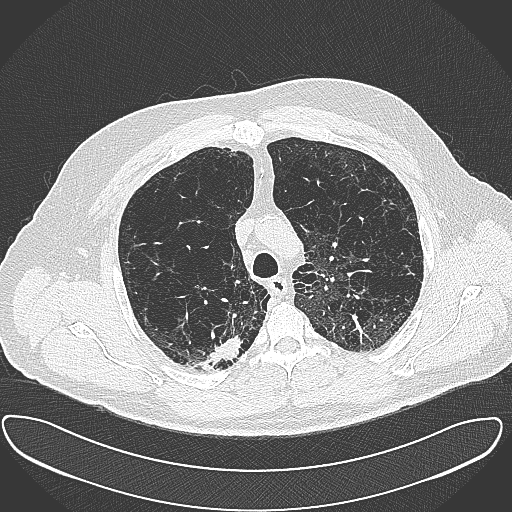
Chest CT (low-dose screening protocol), one axial image, baseline annual screen, lung window (W 1500 / L -600 HU), 1 mm slice thickness, lung (sharp) reconstruction kernel (B80f), slice 90 of 385 in the series. Male participant, aged 60 years at enrolment. Current smoker at enrolment.
Expert reader's lesion annotation, box from (x=195, y=327) to (x=247, y=374) px. Reader record for this screening exam (exam-level; its link to the box is not recorded): non-calcified nodule or mass ≥4 mm, right upper lobe, 15 × 25 mm, spiculated (stellate) margins, soft tissue attenuation. Later outcome: lung cancer diagnosed 32 days after this screen — carcinoma, NOS, right upper lobe, moderately differentiated (G2), stage IB (AJCC 6th edition), 35 mm at pathology.